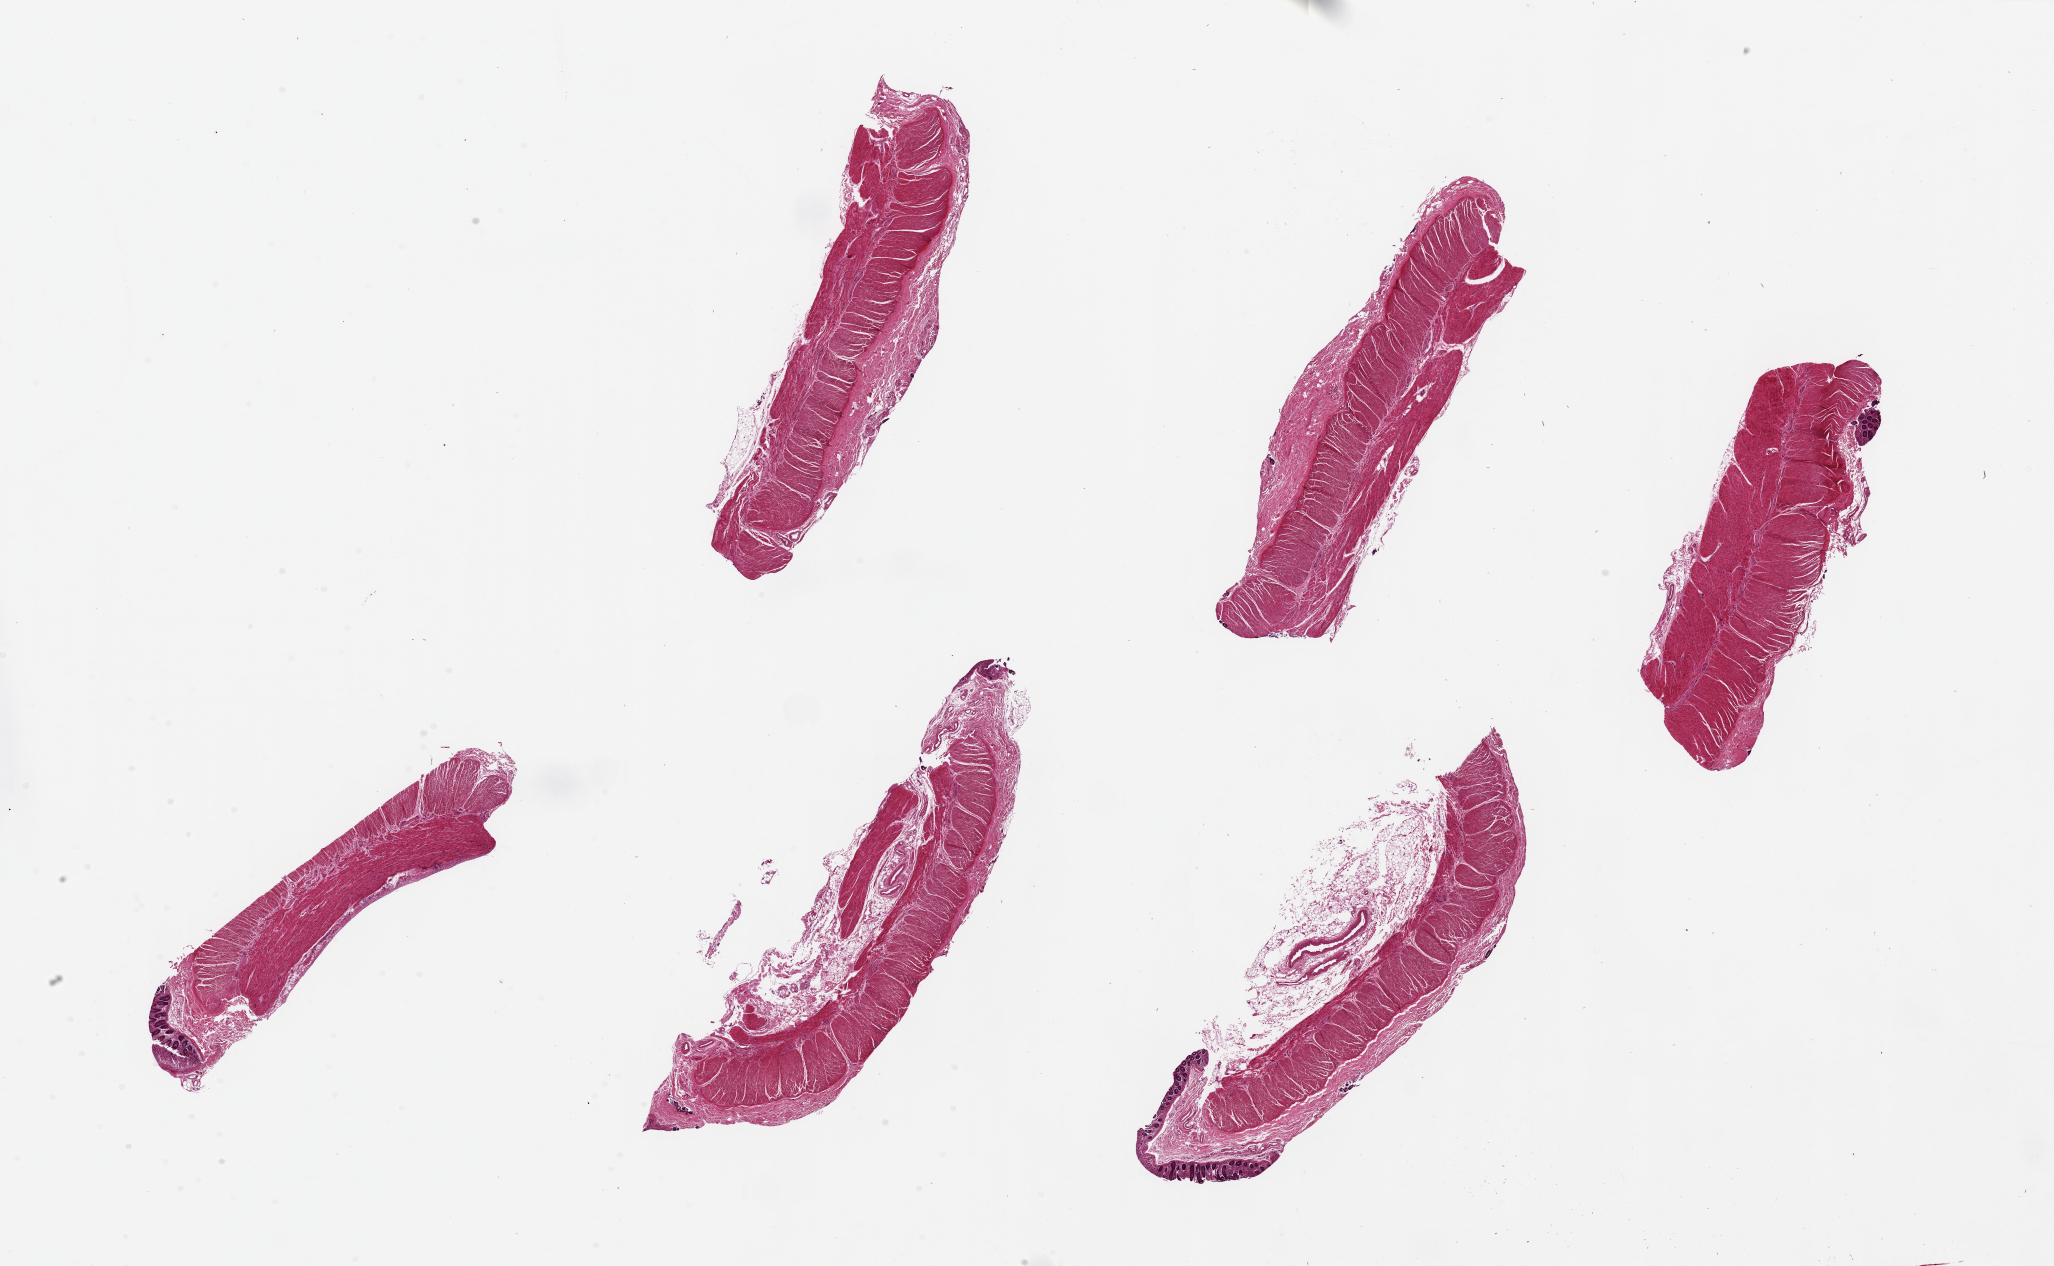
H&E whole-slide image, brightfield, a low-resolution overview of the entire scanned area, about 32.5 x 20.0 mm. PAXgene-fixed paraffin-embedded (PFPE) section. Section of sigmoid colon (target tissue). Donor tissue sample. Female donor.
Review note (as recorded): 6 pieces, up to 9x3mm; mainly muscle (our target) but 3 have foci of mucosa at one pole.